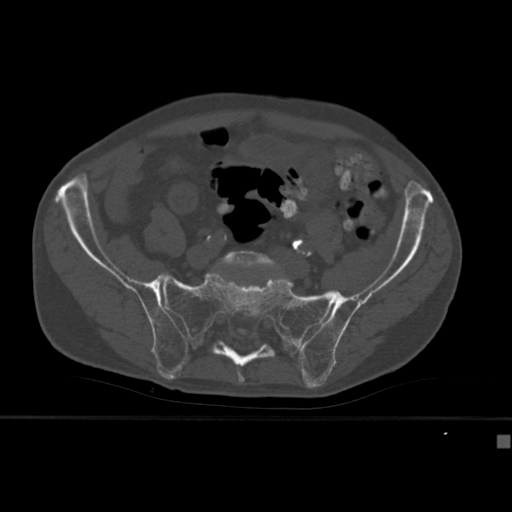
CT including the spine, one axial slice. Slice 68 of 430 in the series (ordered by position). Reconstruction kernel Br40s. 120 kVp. Bone window (W 1800 / L 400 HU). 1.5 mm slice thickness. 512 × 512 image matrix. Patient: male, 64 years. From the clinical record (not read from this slice): primary cancer: uterus; vertebrae with lytic lesions (as recorded): T1, T4, T5, T7, L5.
Outlined on this slice (semi-automatically segmented with operator editing):
- L5 vertebra: bounding box <219,251,280,270> (left, top, right, bottom; pixels)